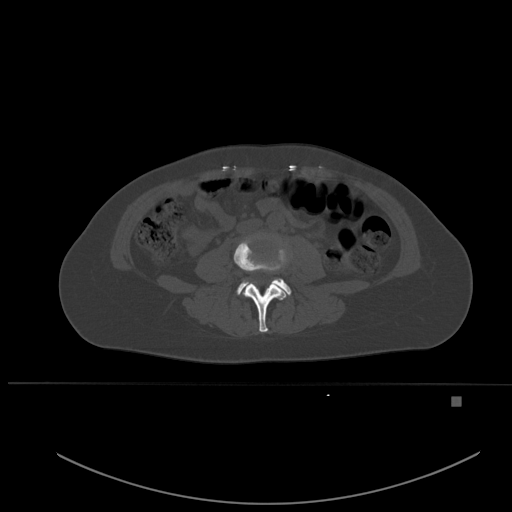
CT including the spine, one axial slice. Slice 185 of 651 in the series (ordered by position). Bone window (W 1800 / L 400 HU). 512 × 512 image matrix, field of view 443 × 443 mm. Female patient, age 49 years. From the clinical record (not read from this slice): primary cancer: breast; vertebrae with lytic lesions (as recorded): L3, T12, L4.
Outlined on this slice (semi-automatically segmented with operator editing):
- L3 vertebra: bounding box (x1, y1, x2, y2) in pixels: (234, 236, 288, 332)
- L4 vertebra: (237, 278, 291, 295)